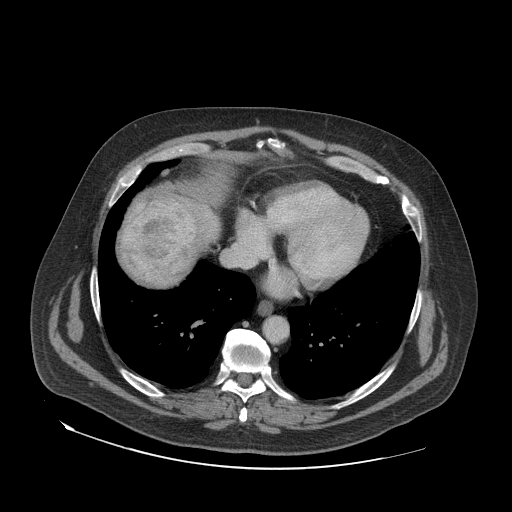
Contrast-enhanced abdominal CT (liver protocol), one axial slice; position 71 of 79 along the scan axis; soft-tissue window (W 400 / L 40 HU); 512 × 512 image matrix. From the clinical record (not read from this slice): diagnosis: hepatocellular carcinoma (patient treated with transarterial chemoembolisation; whether this scan precedes or follows treatment is not stated here); TNM stage (as recorded): Stage-IVA; Child-Pugh class: A; tumour differentiation: well differentiated; tumour nodularity: multinodular.
Outlined on this slice (semi-automatically segmented with operator editing):
- liver parenchyma outside the tumour (the mass and vessels are separate outlines, so this box may not span the whole liver): bounding box [x1, y1, x2, y2] px = [122, 196, 220, 286]
- mass: [122, 195, 197, 284]